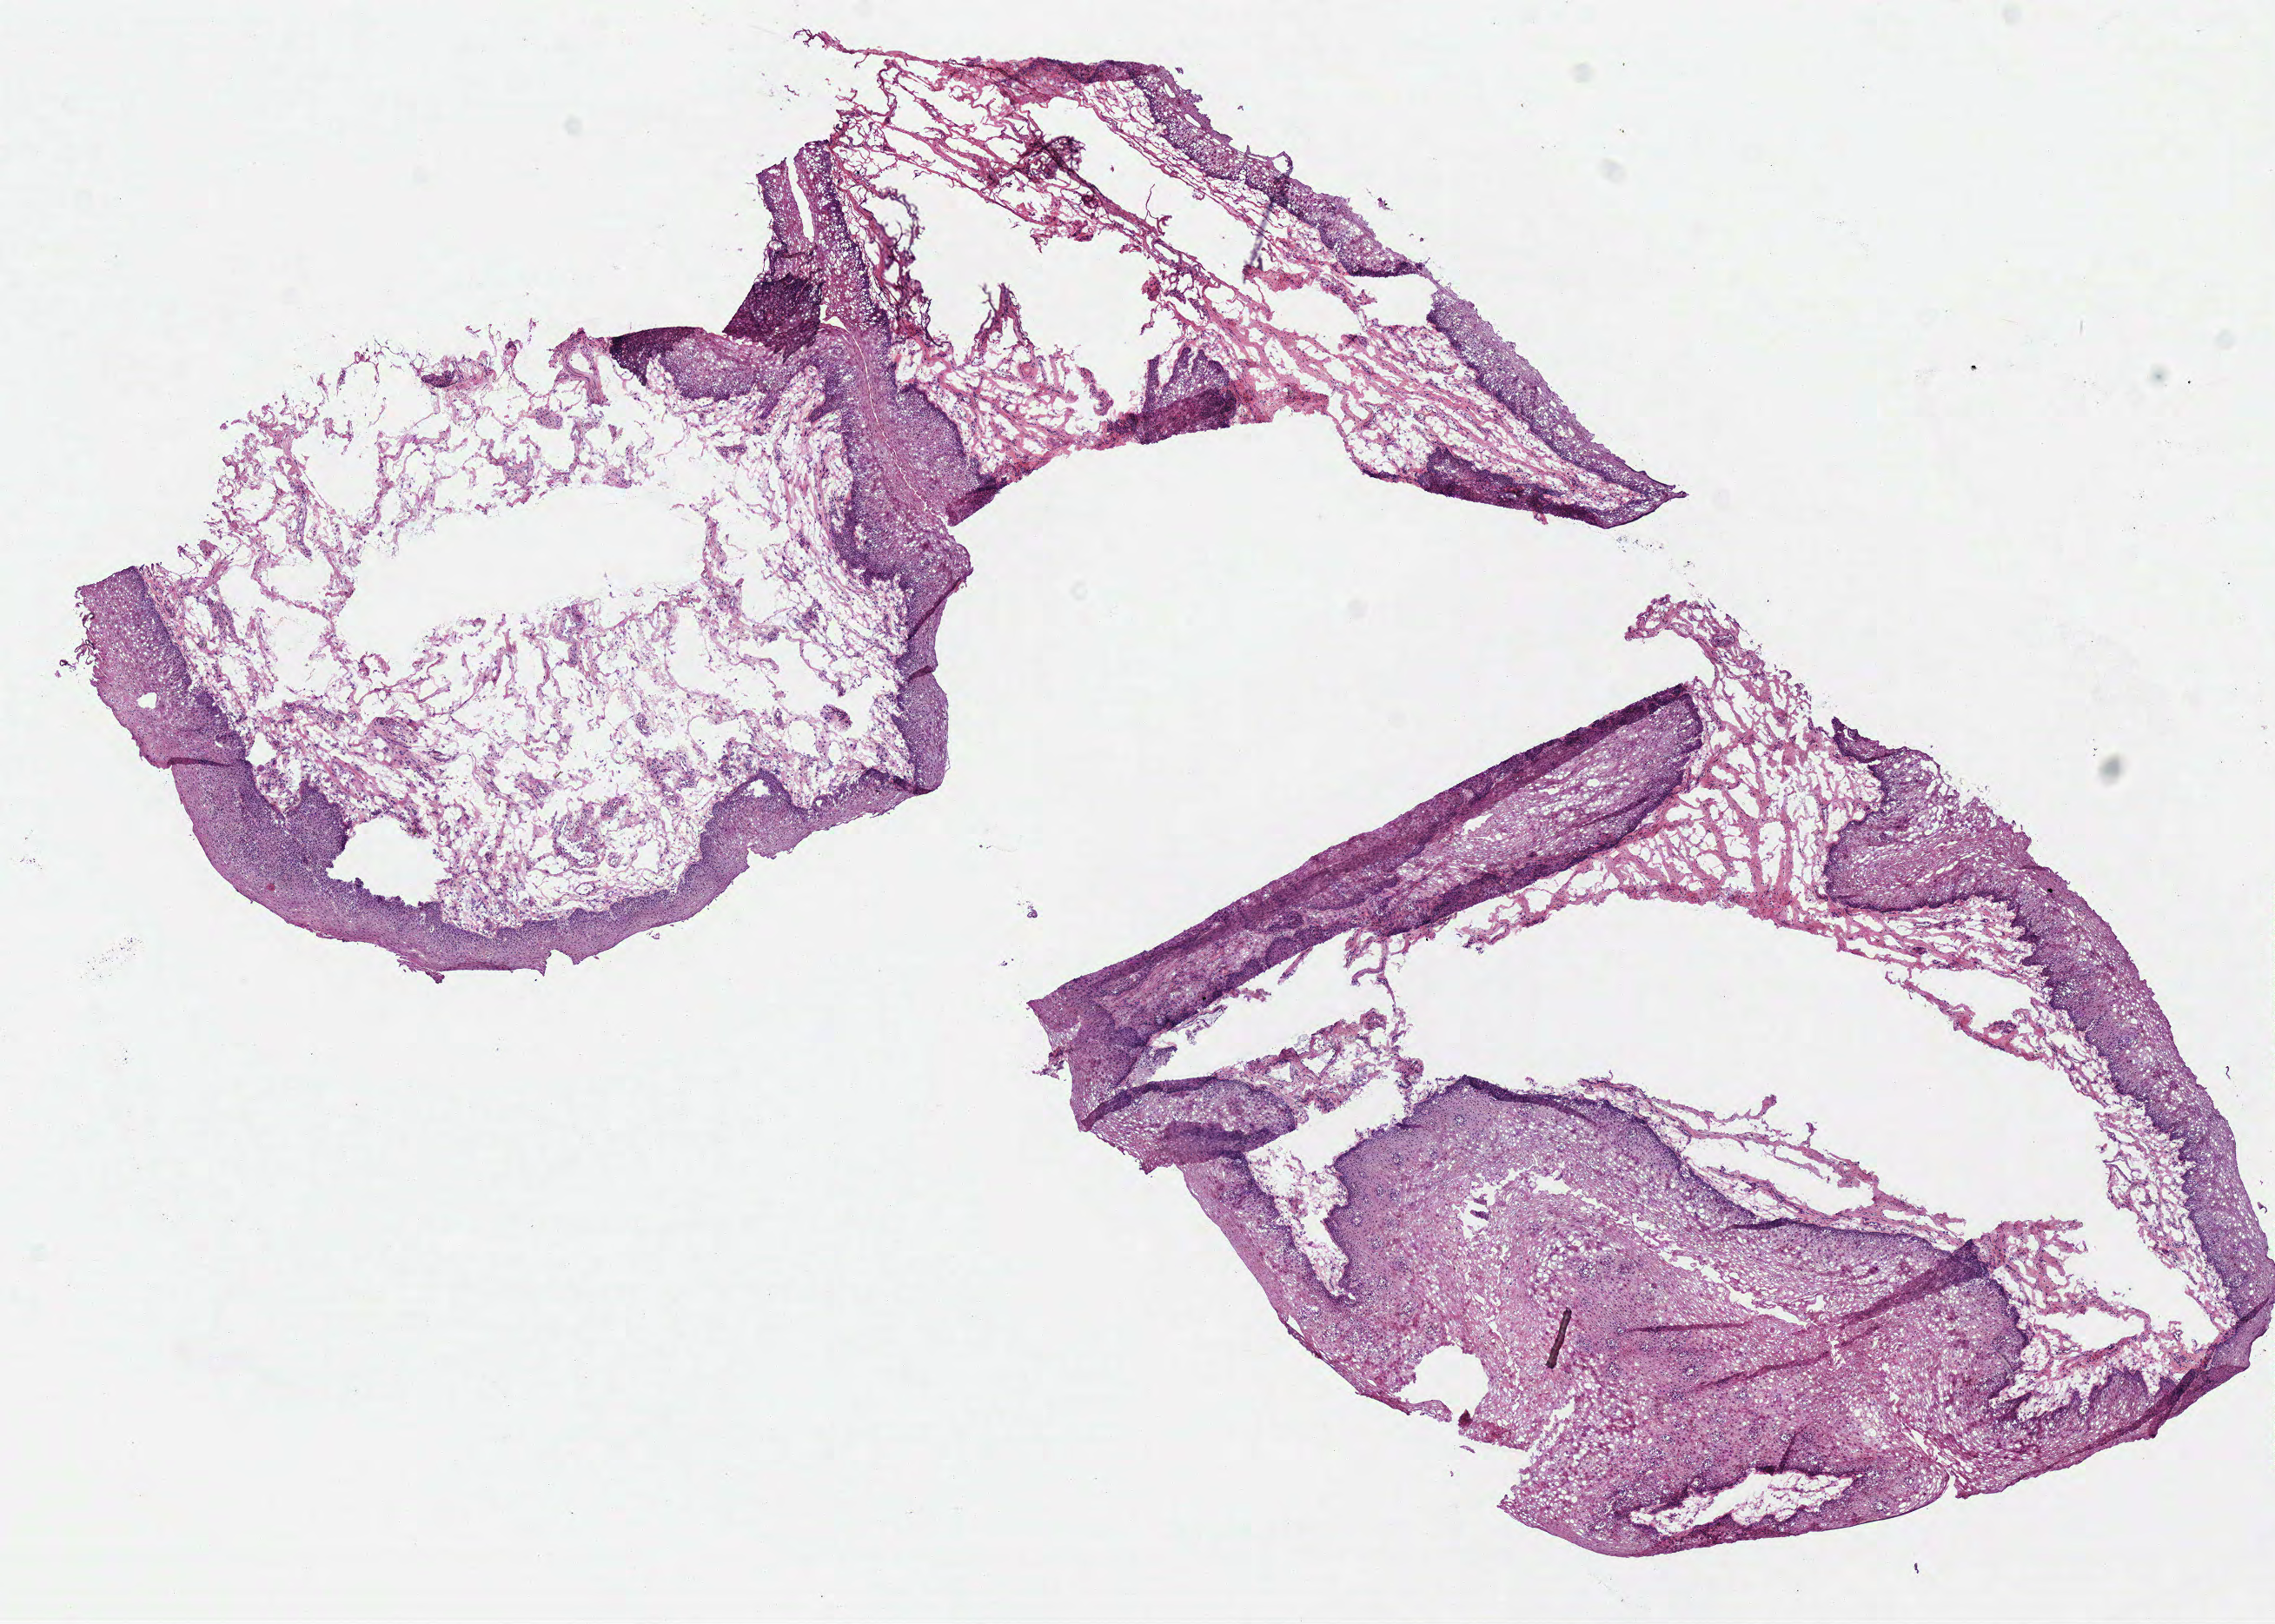
Whole-slide histology image, H&E-stained, a low-resolution overview of the entire scanned area, about 10.3 x 7.4 mm (slide scanned at 40x), frozen section, head and neck, solid tissue normal (non-tumour tissue) sample. Male, age 52 years at initial diagnosis.
This section: solid tissue normal sample (biorepository sample class). Patient diagnosis: Squamous cell carcinoma, NOS (overlapping lesion of lip, oral cavity and pharynx).